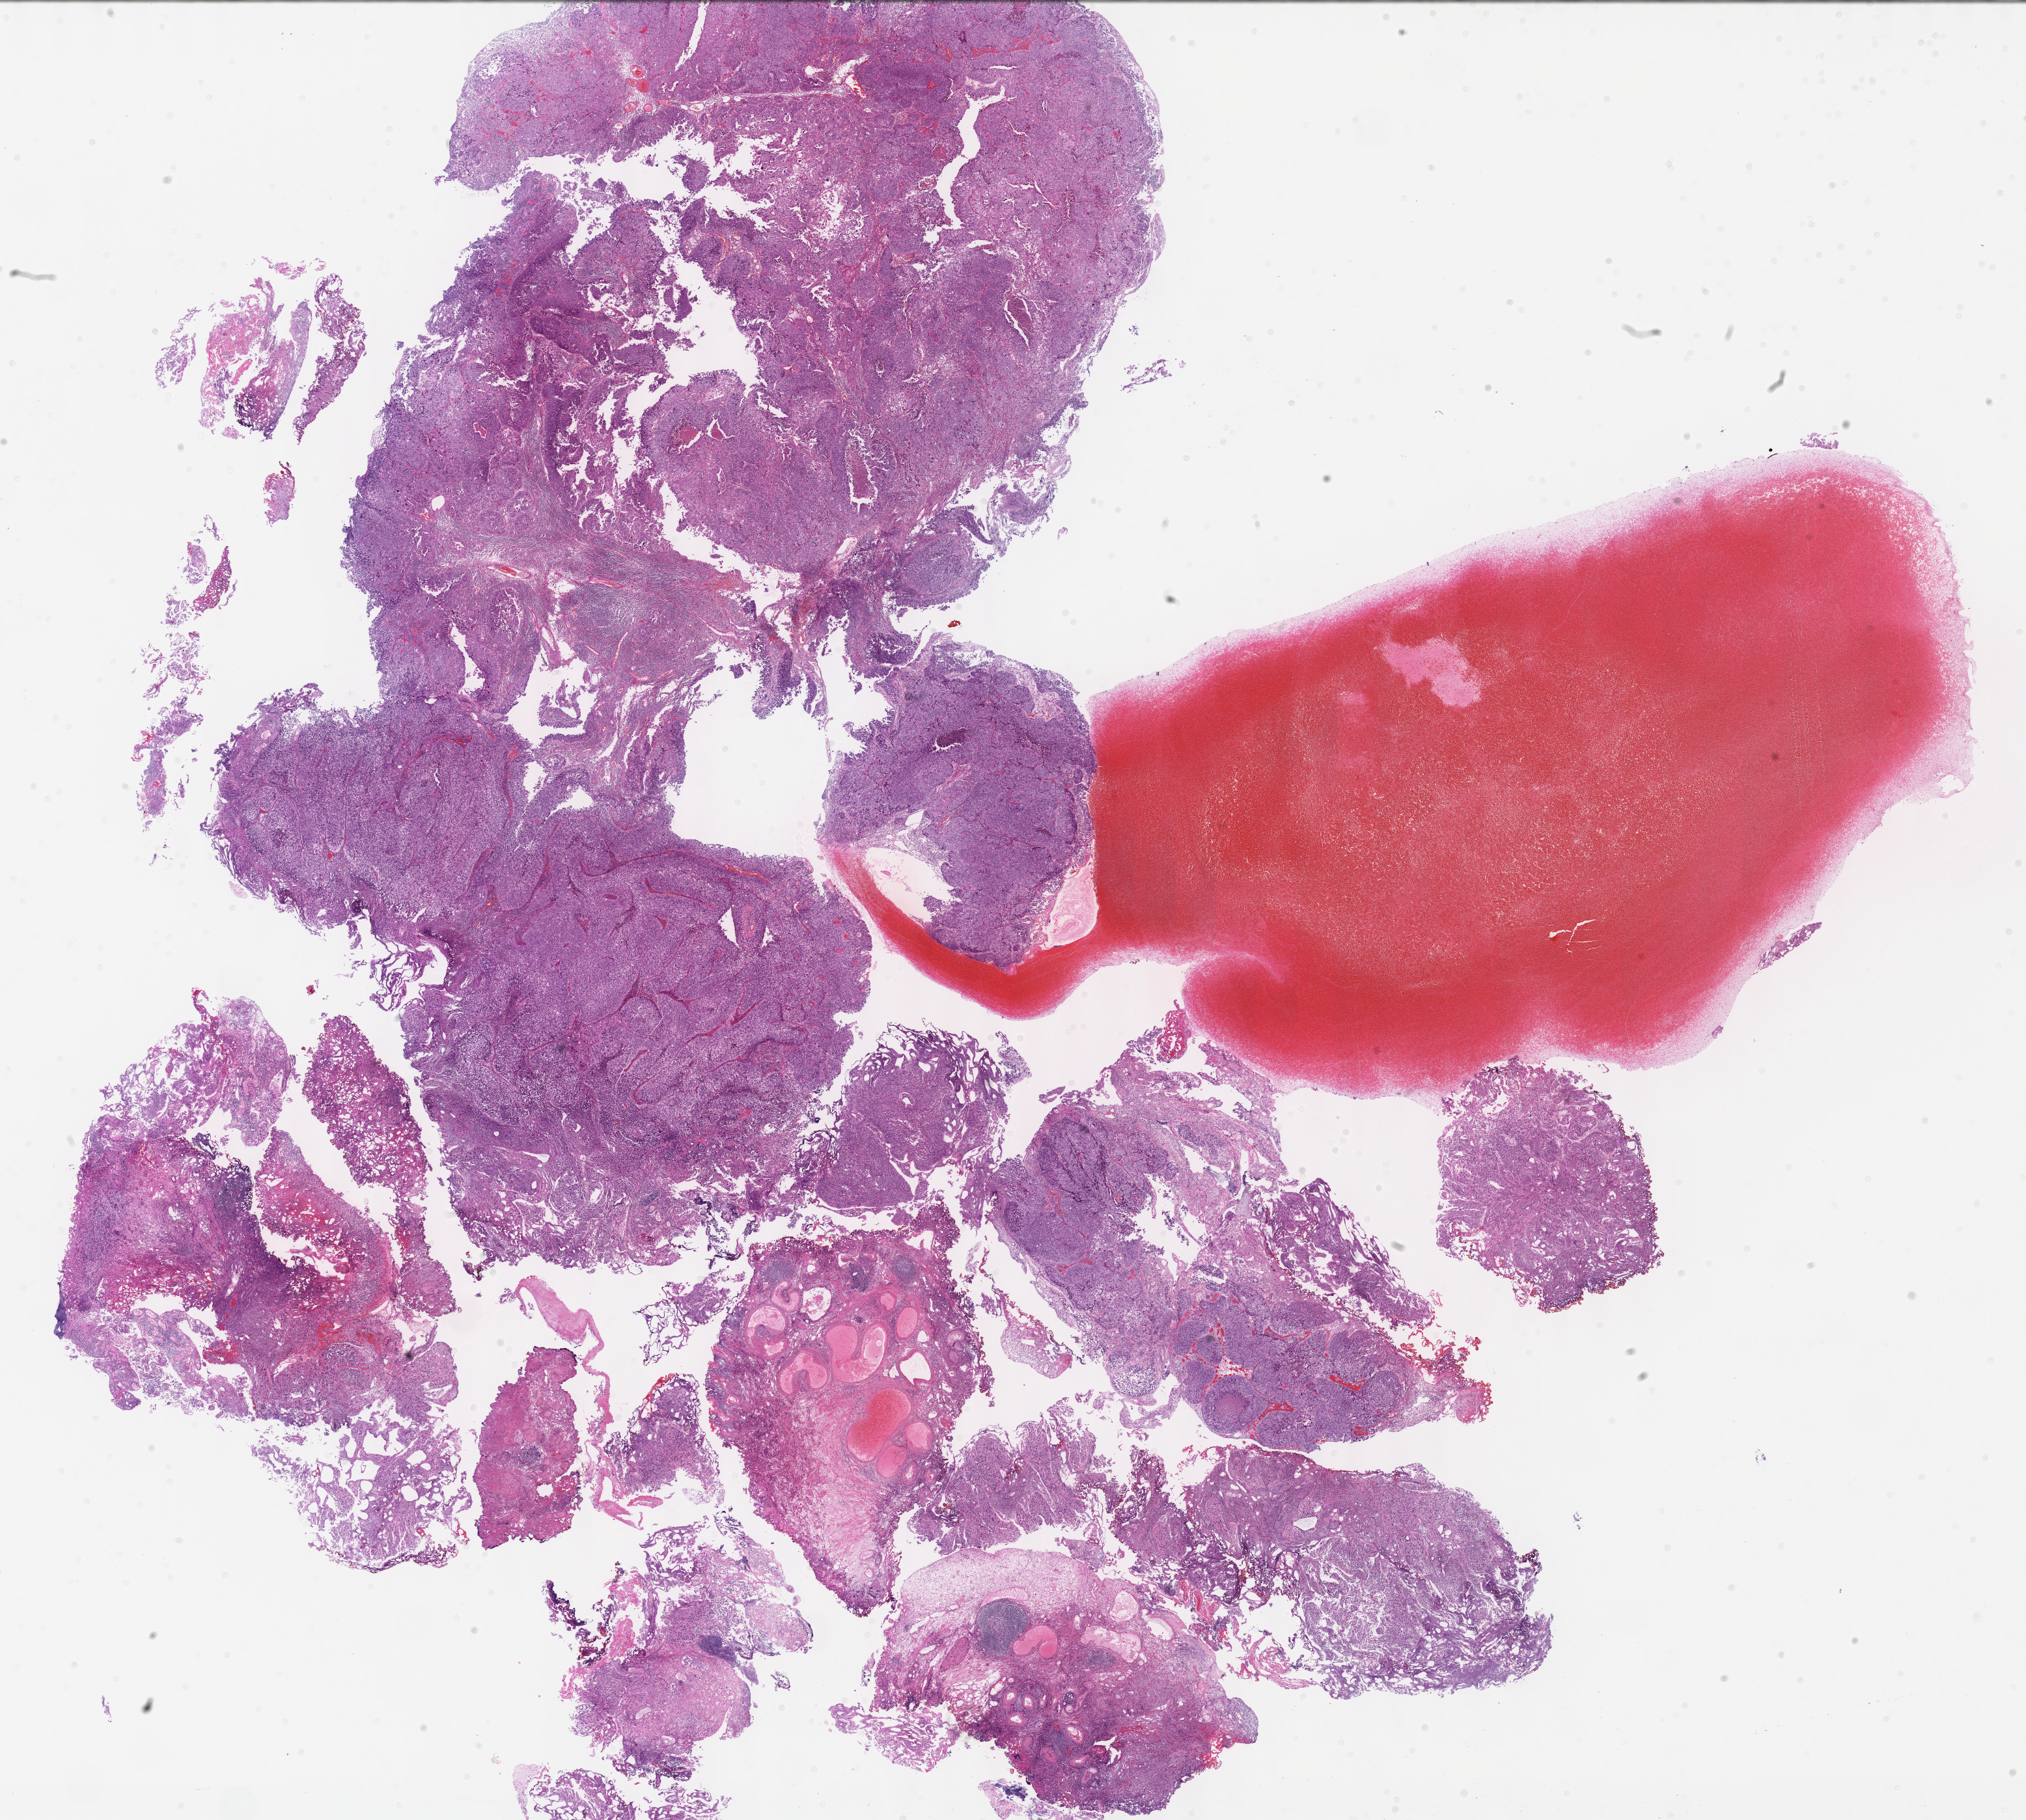
Digitized H&E tissue section (whole slide), shown as a low-resolution overview of the whole scanned area (about 25.1 x 22.6 mm, slide scanned at 40x); FFPE section; primary tumour sample from the bladder. Female, age 75 years at initial diagnosis. Histologic grade: high grade.
* histologic diagnosis: Transitional cell carcinoma
* AJCC pathologic stage: II (6th edition)
* TNM: T2 N0 M0